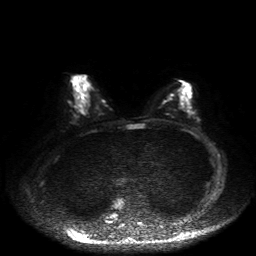
Breast MRI, one axial slice. Slice 27 of 50 in the series (ordered by position). Diffusion-weighted series; image 2 of 4 stored at this slice position (different b-values; order by instance number). 1.5 T. 256 × 256 image matrix. Female patient.
Annotated regions visible in this slice (outlined manually by an expert reader):
- tumour on diffusion-weighted imaging: bounding box (x1, y1, x2, y2) in pixels: (76, 103, 82, 111)